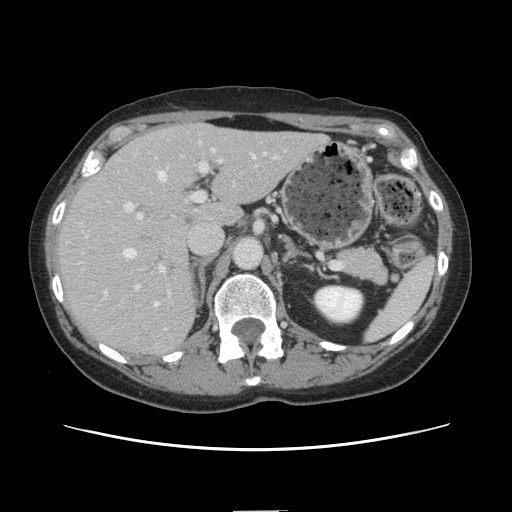
Contrast-enhanced abdominal CT, one axial slice; slice 86 of 141 in the series (ordered by position); 120 kVp; intravenous contrast given; soft-tissue window (W 400 / L 40 HU); 2.5 mm slice thickness; 512 × 512 image matrix, field of view 350 × 350 mm. Female patient, age 63 years. From the clinical record (not read from this slice): diagnosis: colorectal cancer liver metastases, imaged before liver resection; multiple liver metastases: yes; largest metastasis: 3.2 cm.
Structures marked on this image (manually delineated by an expert):
- hepatic veins: box from (x=105, y=156) to (x=255, y=307) px
- liver: (x=58, y=124)–(x=325, y=356)
- planned liver remnant (the part of the liver to remain after resection): (x=177, y=124)–(x=325, y=226)
- portal vein (with intrahepatic branches): (x=124, y=153)–(x=255, y=297)
- liver metastasis: (x=167, y=263)–(x=176, y=273)